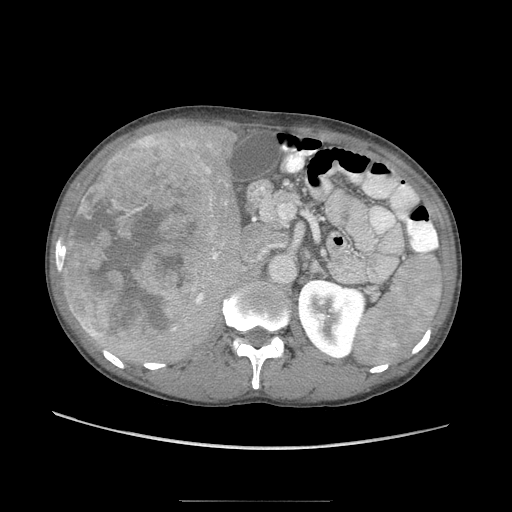
Contrast-enhanced abdominal CT (liver protocol), one axial slice; slice 42 of 103 in the series (ordered by position); soft-tissue window (W 400 / L 40 HU); 512 × 512 image matrix. From the clinical record (not read from this slice): diagnosis: hepatocellular carcinoma (patient treated with transarterial chemoembolisation; whether this scan precedes or follows treatment is not stated here); TNM stage (as recorded): Stage-IIIA; Child-Pugh class: A; tumour differentiation: moderately differentiated; tumour nodularity: multinodular.
Outlined on this slice (semi-automatically segmented with operator editing):
- liver parenchyma outside the tumour (the mass and vessels are separate outlines, so this box may not span the whole liver): bounding box (x1, y1, x2, y2) in pixels: (62, 124, 250, 365)
- mass: (63, 132, 220, 347)
- liver vessels: (82, 145, 207, 329)